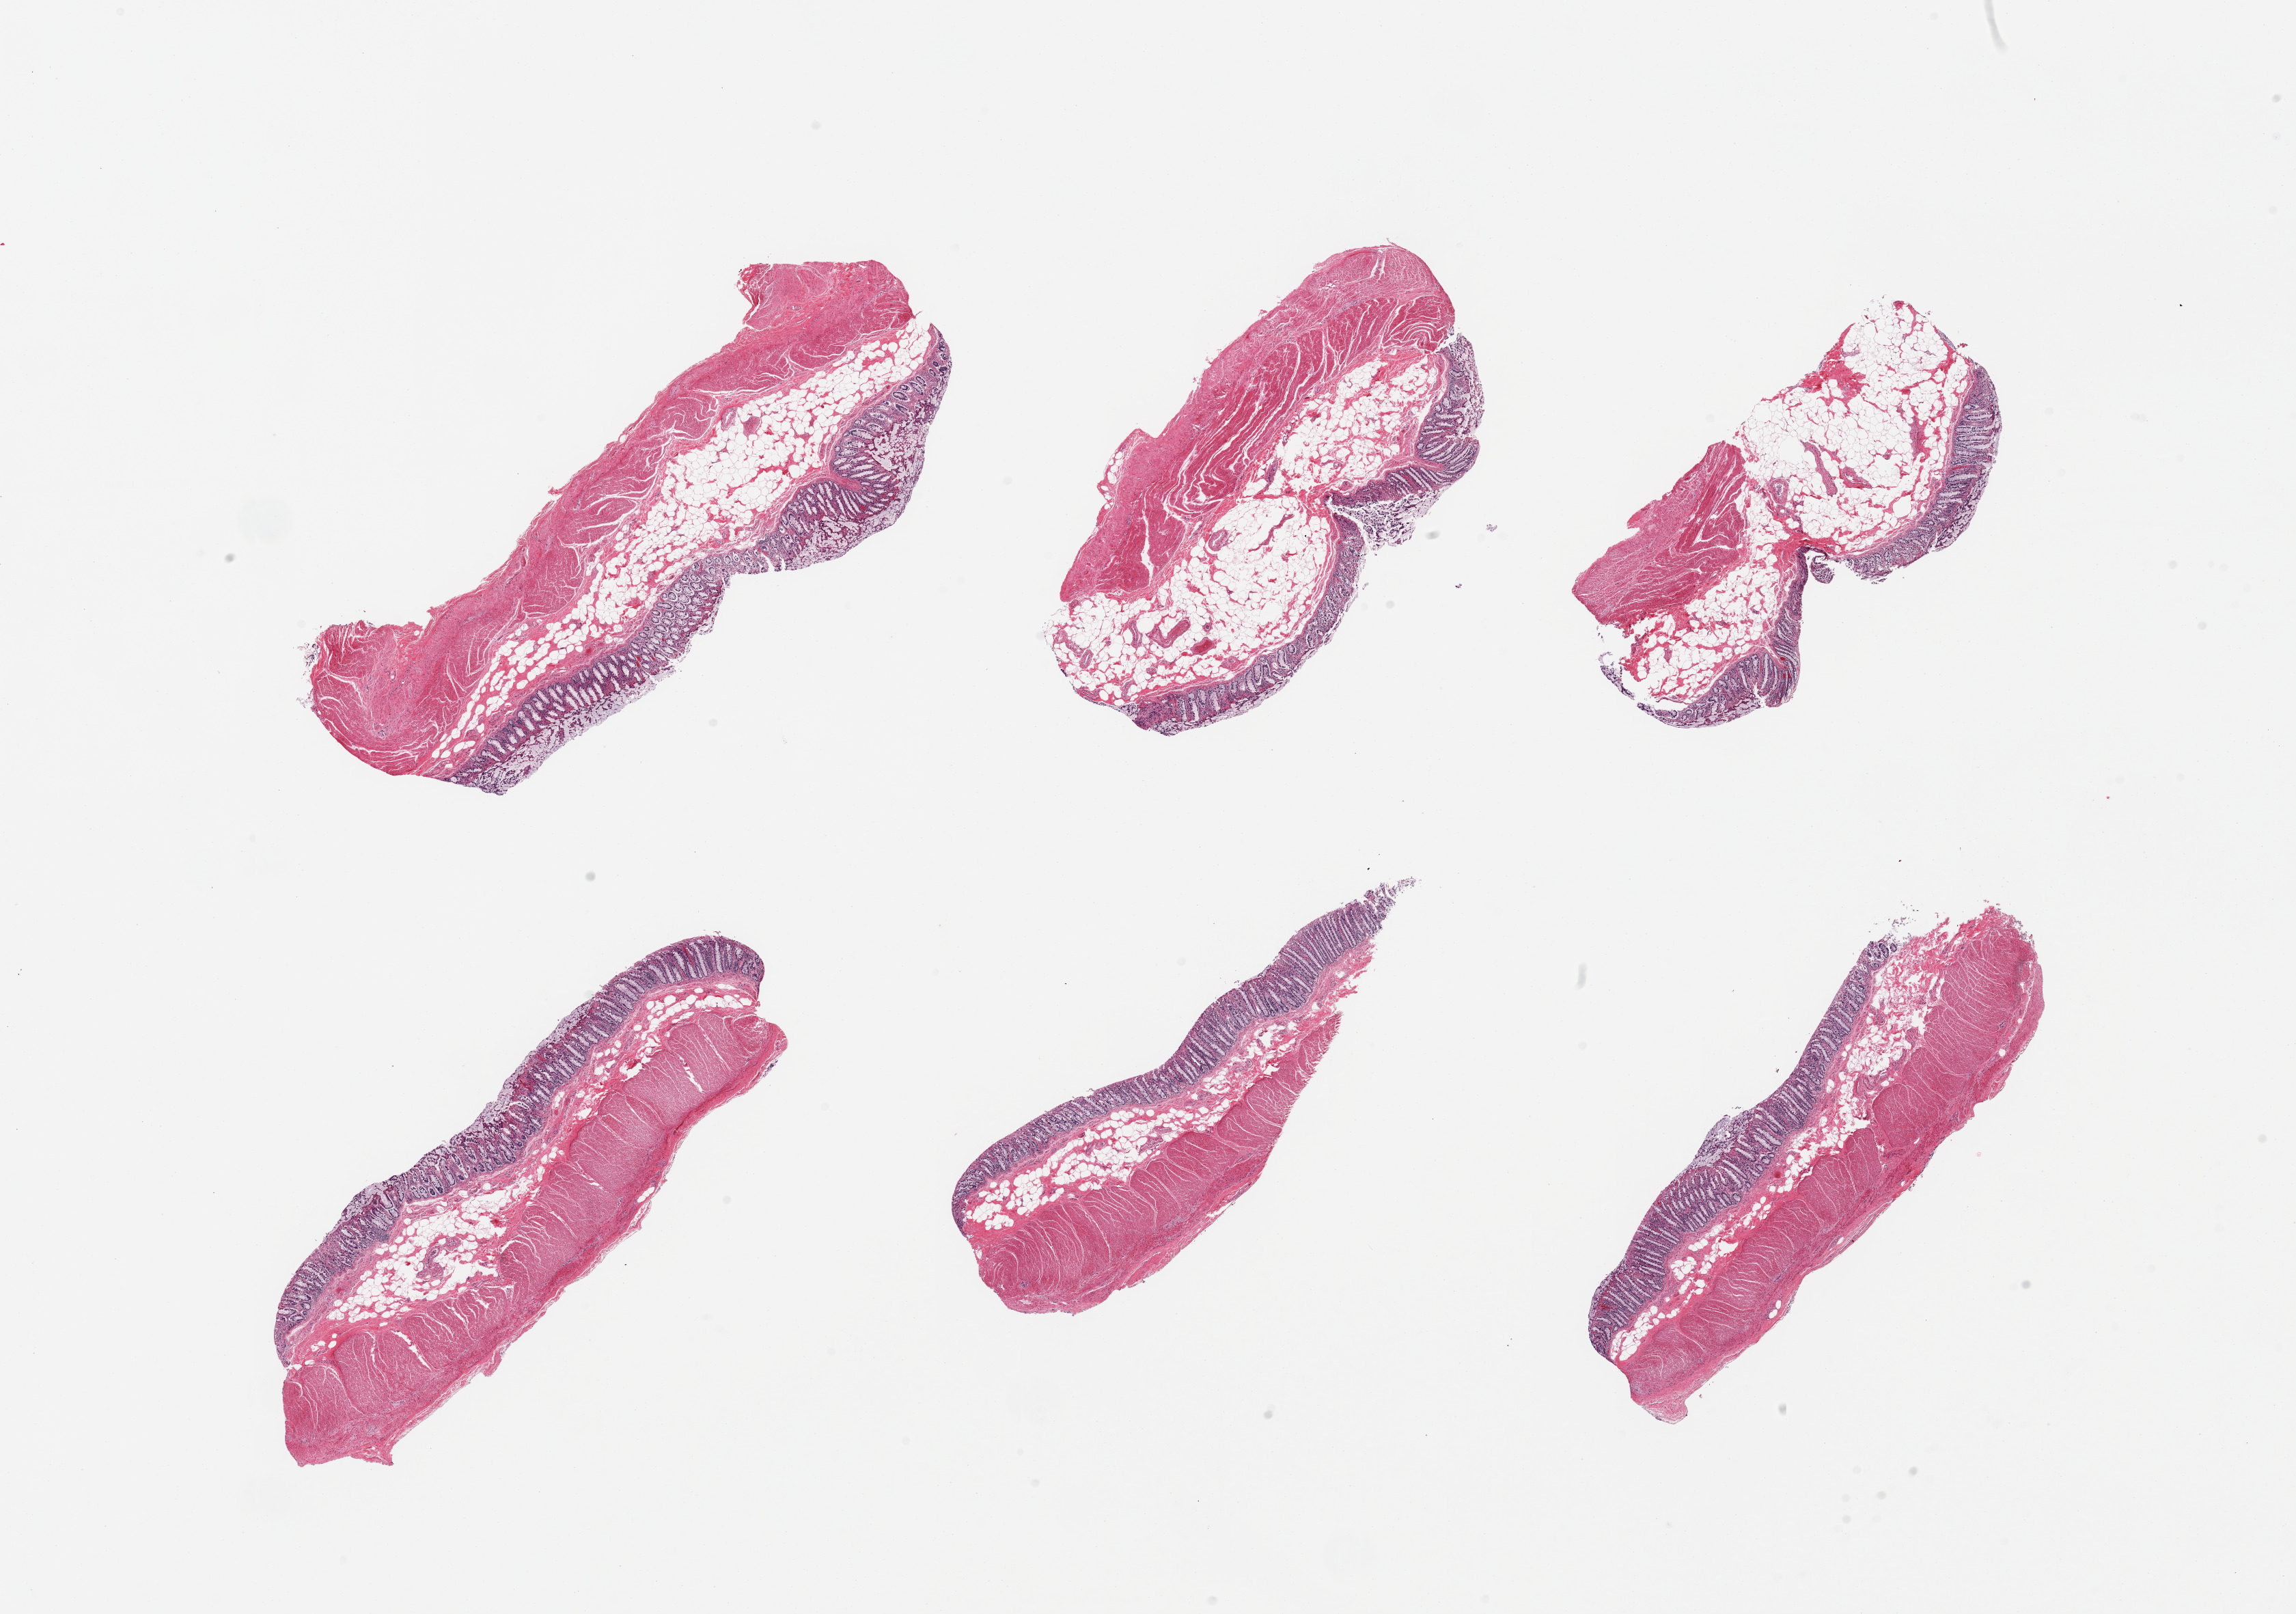
Whole-slide image, haematoxylin and eosin stain, a low-resolution overview of the entire scanned area, about 26.6 x 18.7 mm (slide scanned at 20x). PAXgene-fixed, paraffin-embedded tissue. Sampled site (target tissue): transverse colon. Donor tissue sample.
Review note (as recorded): 6 pieces, mucosa ~0.25mm, ~10-15% thickness, many areas autolysis approached score 3 with sloughing of glandular elements.